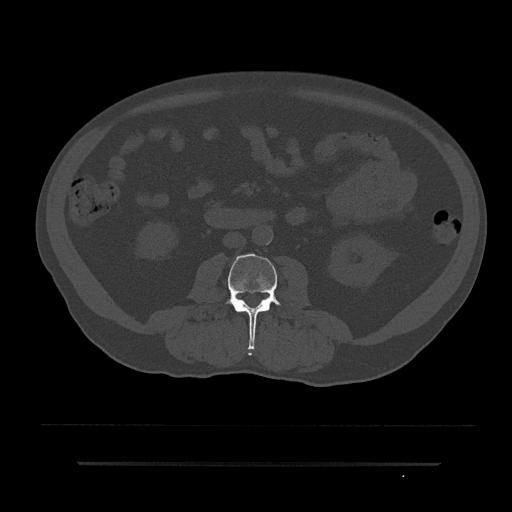
CT including the spine, one axial slice; slice 2 of 797 in the series (ordered by position); reconstruction kernel Br40s/3; 120 kVp; bone window (W 1800 / L 400 HU); 512 × 512 image matrix, field of view 464 × 464 mm. Male patient, age 59 years. Case-level facts recorded for this patient, not image findings: primary cancer: bile ducts; vertebrae with lytic lesions (as recorded): T10.
Structures marked on this image (semi-automatic segmentation, software-assisted and operator-edited):
- L3 vertebra: box from (x=222, y=254) to (x=288, y=349) px